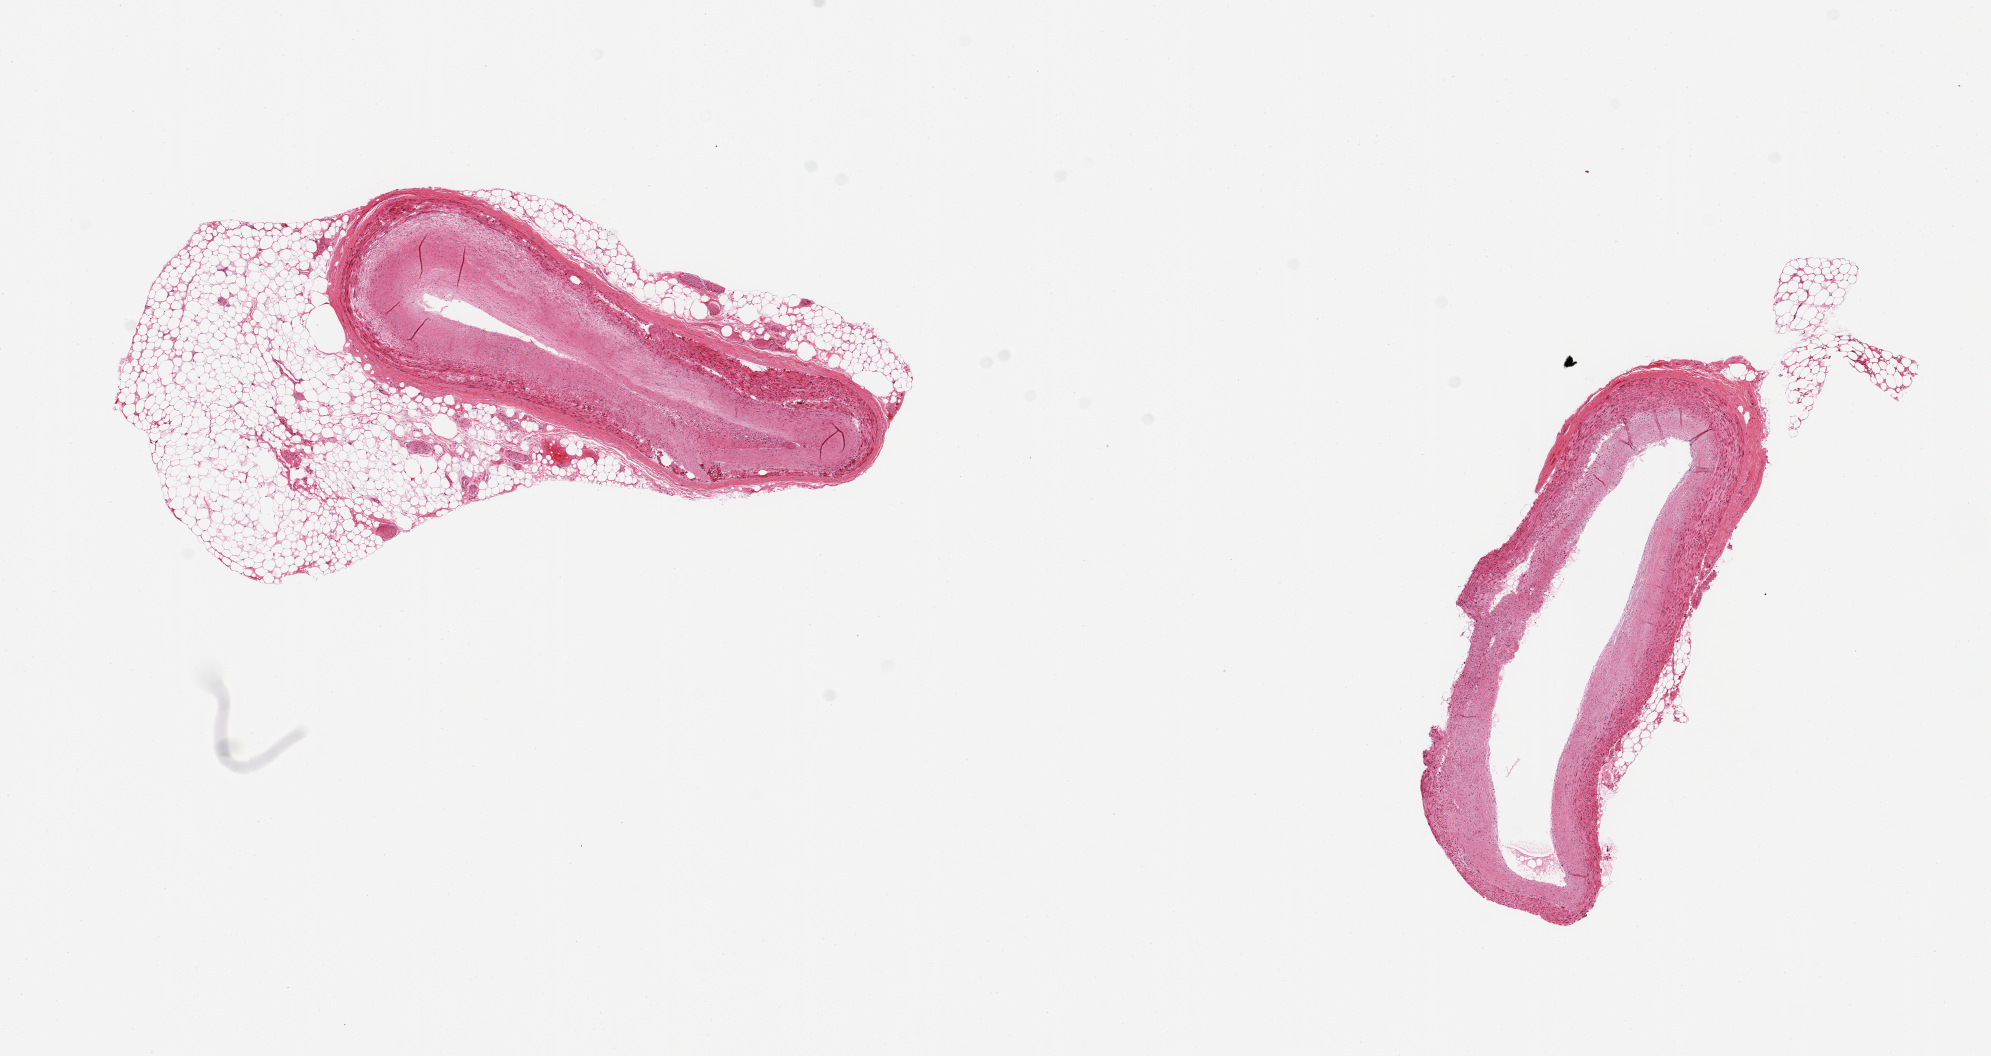
Digitized H&E-stained section, brightfield — low-resolution overview of the scanned area, about 15.8 x 8.4 mm (acquisition: 20x scan), PAXgene-fixed, paraffin-embedded tissue, target tissue: coronary artery, tissue donor sample. Female donor.
• pathologist's review note for this sample: 2 pieces, one piece includes 3 mm attachment of fat (50%), atherosclerosis